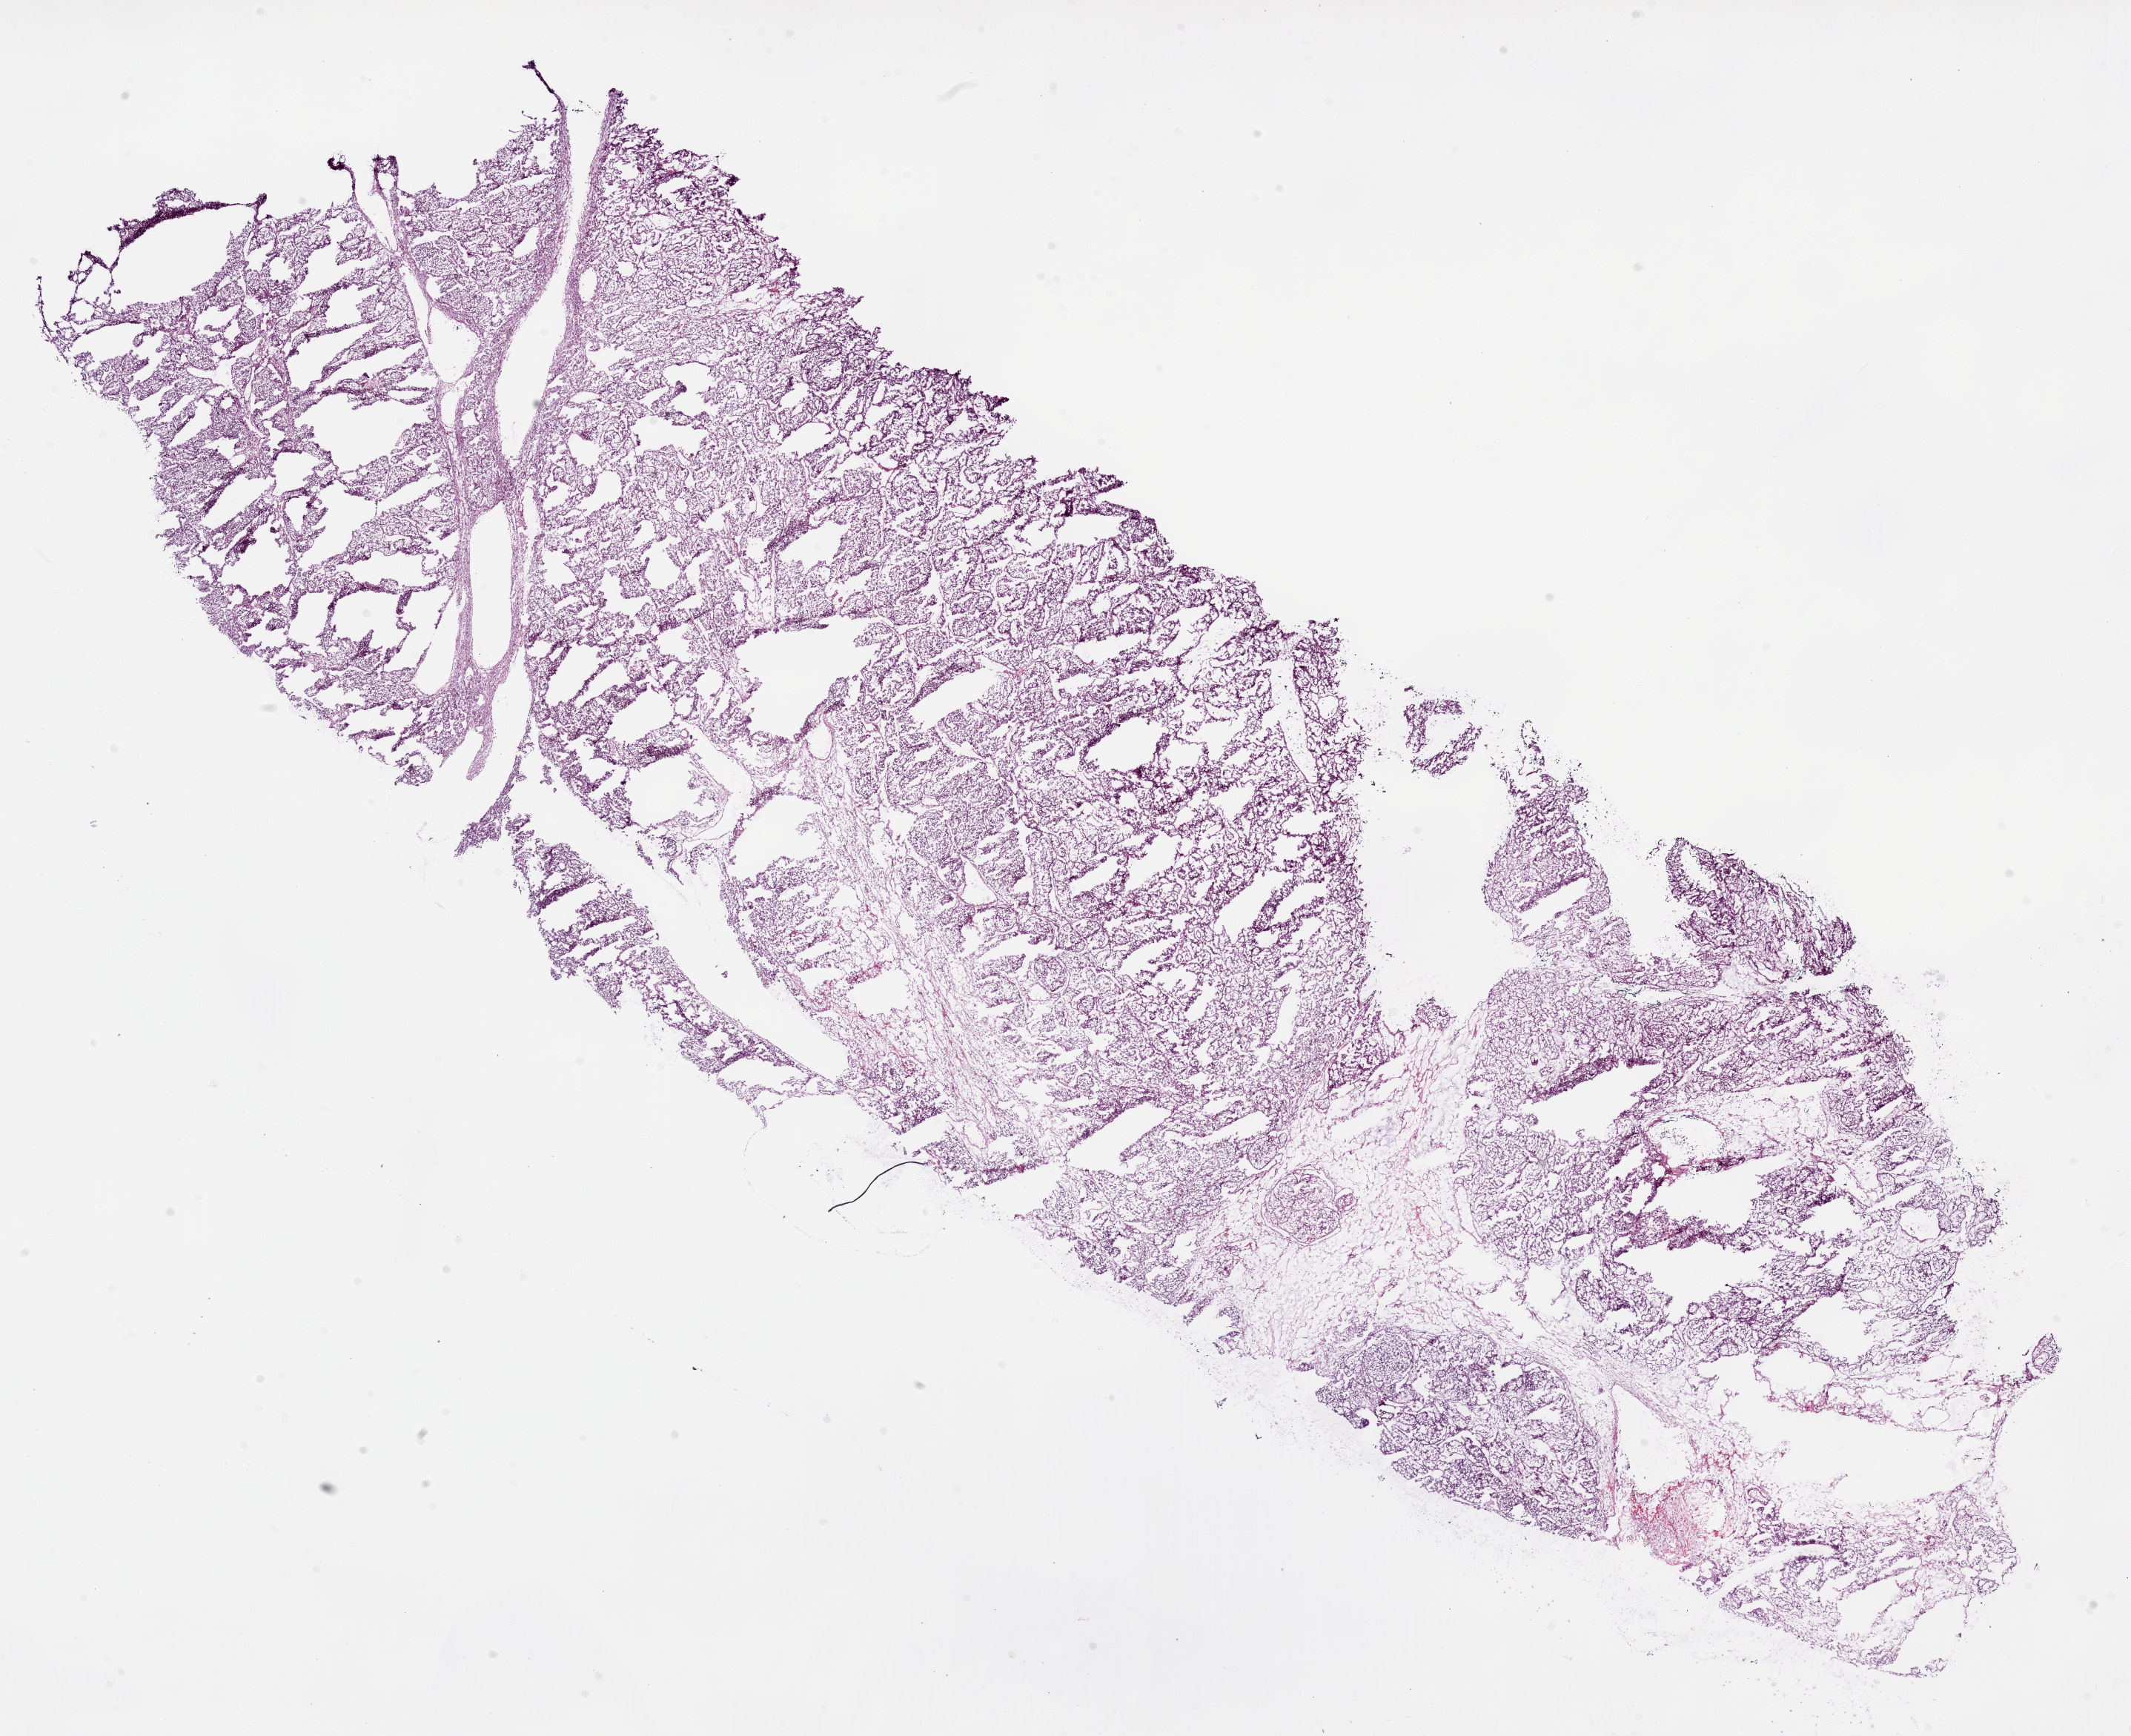
Digitized H&E-stained tissue section (whole slide), shown as a low-resolution overview of the whole scanned area (about 23.1 x 18.8 mm). Frozen section from the bottom of the tissue portion. Primary tumour sample from the kidney. Male patient; age at initial diagnosis 68 years. Histologic grade: G3 (poorly differentiated). Slide review estimates, as recorded: tumour cells 90%, tumour nuclei 85%, normal cells 0%, stromal cells 10%, necrosis 0%.
TNM: T3b NX M0. Diagnosis: Clear cell adenocarcinoma, NOS. AJCC pathologic stage: III.